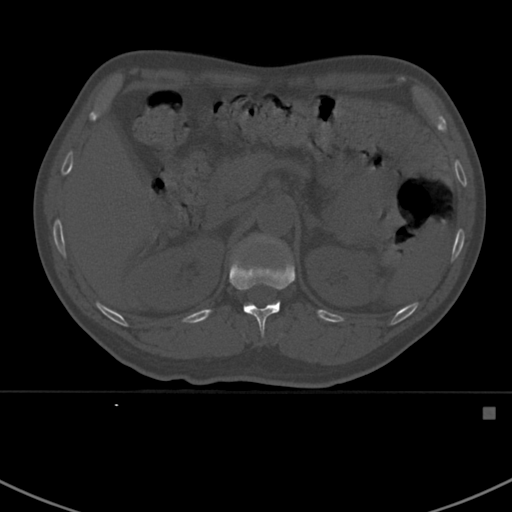
CT including the spine, one axial slice. Slice 325 of 412 in the series (ordered by position). Reconstruction kernel Br40s. 120 kVp. Bone window (W 1800 / L 400 HU). 512 × 512 image matrix. Patient: male, 59 years. Case-level facts recorded for this patient, not image findings: primary cancer: prostate.
Structures marked on this image (semi-automatically segmented with operator editing):
- L1 vertebra: bounding box [x1, y1, x2, y2] px = [247, 234, 282, 247]
- T12 vertebra: [230, 256, 295, 337]